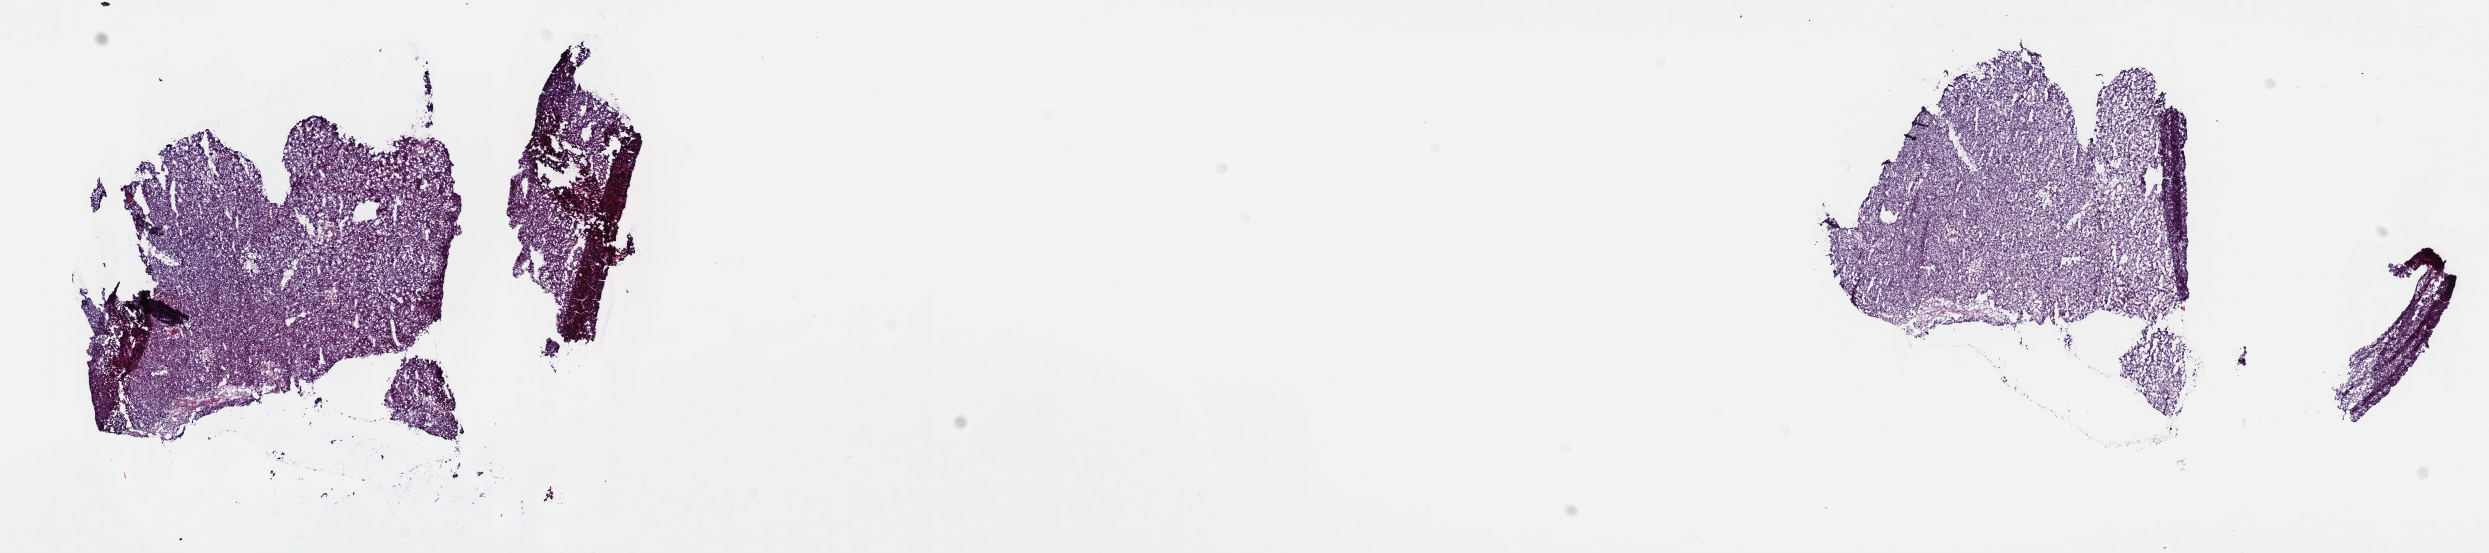
Hematoxylin and eosin (H&E) stained whole-slide image — low-resolution overview of the scanned area, about 20.1 x 4.5 mm (from a 40x scan); frozen section from the top of the tissue portion; liver, primary tumour sample. Male patient; age at initial diagnosis 51 years. Histologic grade: G2 (moderately differentiated). Composition of this section per pathologist review: tumour cells 100%, tumour nuclei 95%, normal cells 0%, stromal cells 0%, necrosis 0%. Infiltration values recorded for this section: lymphocyte infiltration 0%, monocyte infiltration 0%, neutrophil infiltration 0%.
AJCC pathologic stage: I (6th edition). Histologic diagnosis: Hepatocellular carcinoma, NOS.